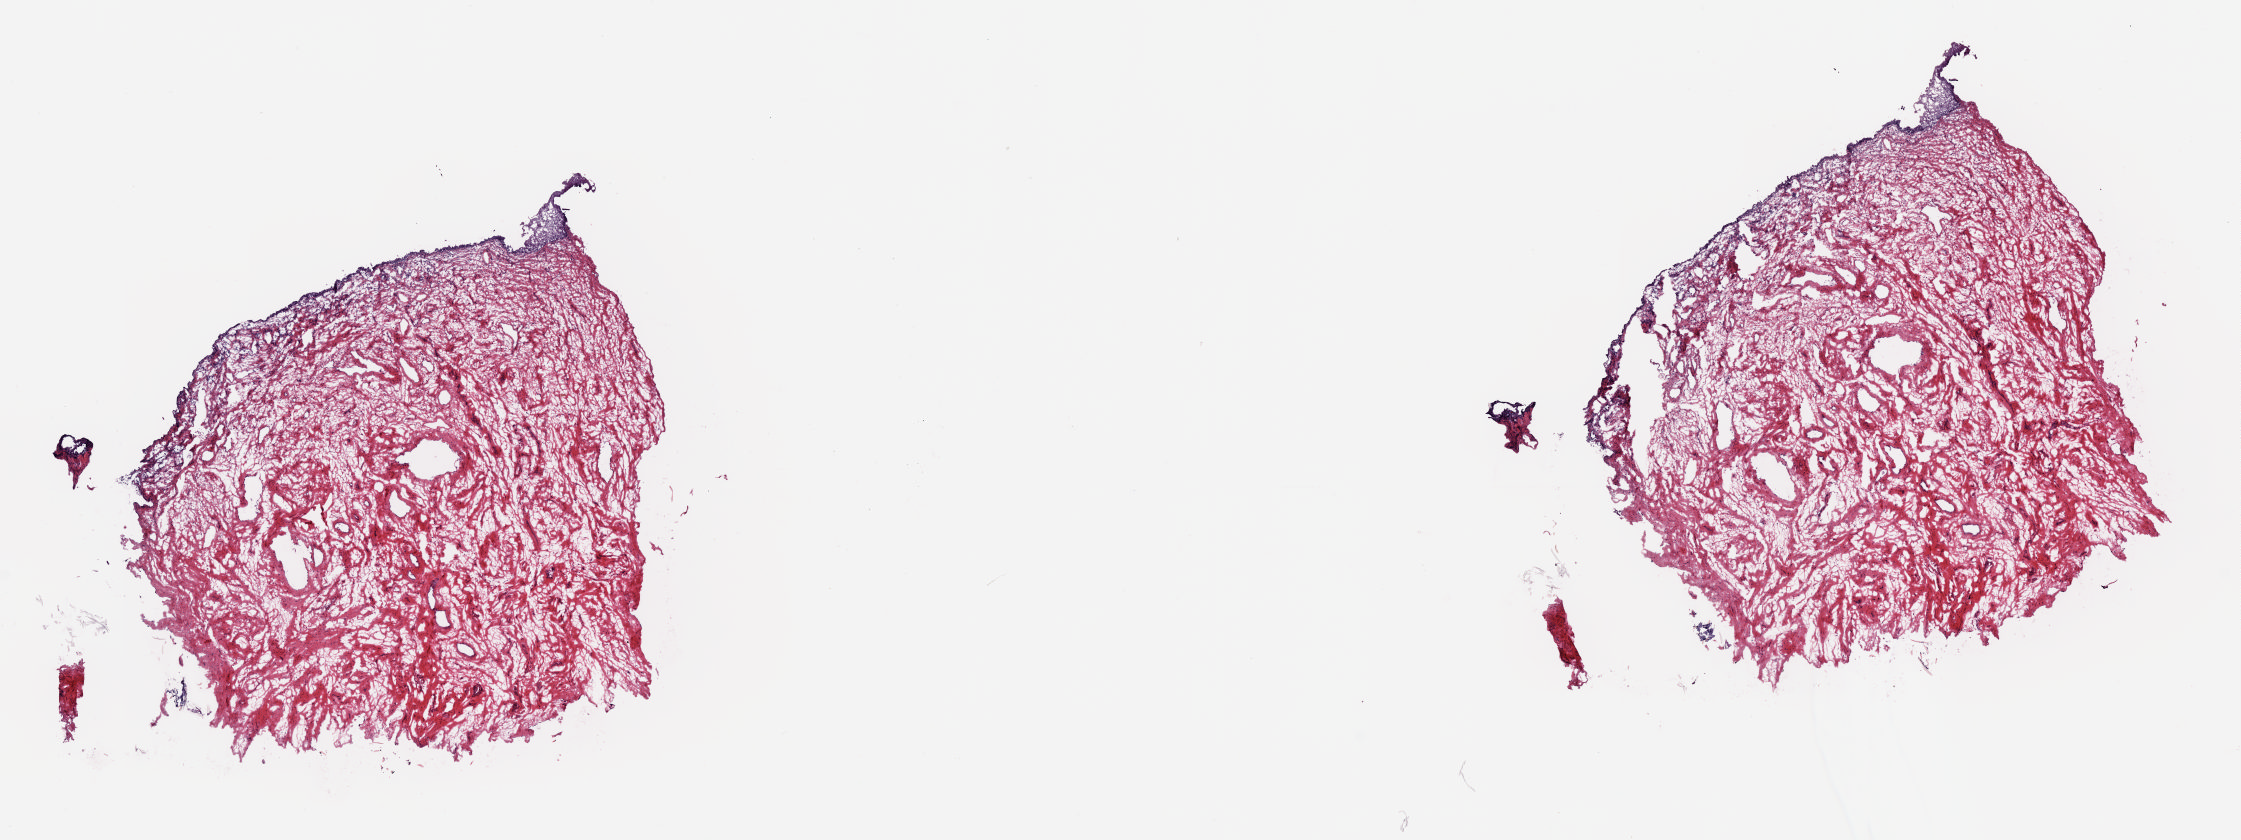
Whole-slide histology image, H&E-stained — a low-resolution overview of the entire scanned area, about 17.7 x 6.6 mm; frozen section from the top of the tissue portion; solid tissue normal (non-tumour tissue) sample from the uterus. Patient: female, age at initial diagnosis 86 years. Slide review estimates, as recorded: tumour cells 0%, tumour nuclei 0%, normal cells 100%, stromal cells 0%, necrosis 0%. Infiltration values recorded for this section: lymphocyte infiltration 0%, monocyte infiltration 0%, neutrophil infiltration 0%.
This section: solid tissue normal sample (biorepository sample class). Patient diagnosis: Serous cystadenocarcinoma, NOS (endometrium).